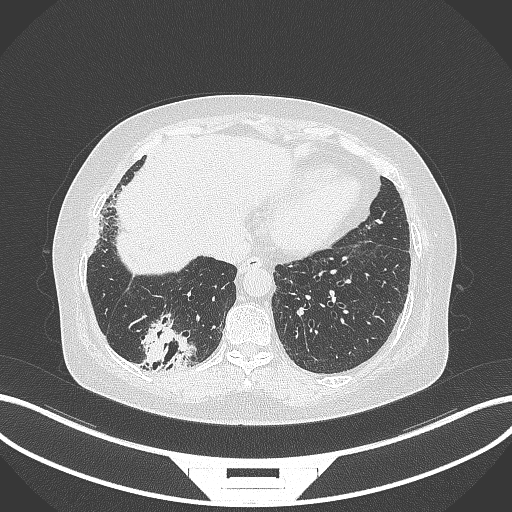
Chest CT, one axial slice; position 47 of 296 along the scan axis; lung window (W 1500 / L -600 HU); 1 mm slice thickness; 512 × 512 image matrix, field of view 400 × 400 mm. Female patient, age 65 years. From the clinical record (not read from this slice): clinical TNM (as recorded): T2b N1 M0.
Annotated regions visible in this slice (bounding box drawn by a radiologist):
- lung tumour (recorded histology: adenocarcinoma): bounding box [x1, y1, x2, y2] px = [137, 309, 200, 372]